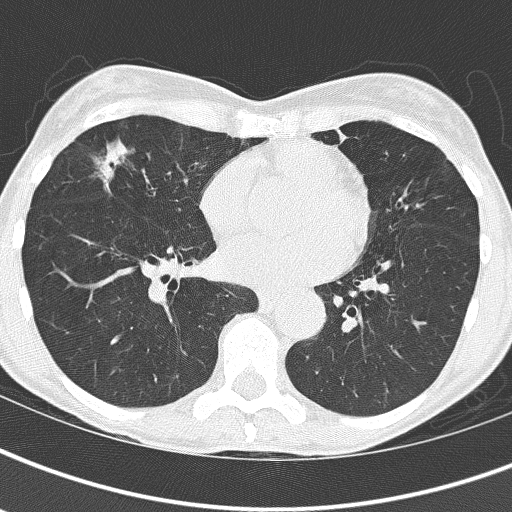
Low-dose screening chest CT, axial slice. Baseline screening round. Lung window (W 1500 / L -600 HU). 2 mm slice thickness. Slice 95 of 161 in the series. Female, age 67 years at enrolment. Current smoker at enrolment.
Expert reader's lesion annotation, bounding box (x1, y1, x2, y2) in pixels: (87, 130, 177, 211). Screening reader's record for this exam: no non-calcified nodule ≥4 mm recorded. Official screen result: negative screen, significant abnormalities not suspicious for lung cancer. Later outcome: lung cancer diagnosed 832 days after this screen — bronchiolo-alveolar adenocarcinoma, NOS, right middle lobe, well differentiated (G1), stage IA (AJCC 6th edition), 25 mm at pathology.